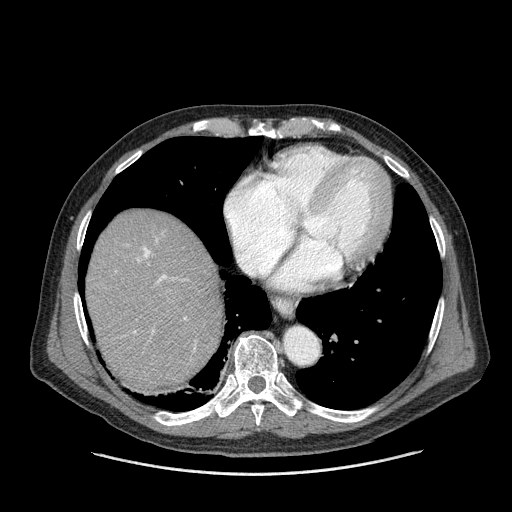
Contrast-enhanced abdominal CT (liver protocol), one axial slice; position 138 of 180 along the scan axis; 120 kVp; one of 2 acquisitions stored at this slice position; soft-tissue window (W 400 / L 40 HU); 2.5 mm slice thickness; 512 × 512 image matrix, field of view 420 × 420 mm. From the clinical record (not read from this slice): diagnosis: hepatocellular carcinoma (patient treated with transarterial chemoembolisation; whether this scan precedes or follows treatment is not stated here); TNM stage (as recorded): Stage-II; Child-Pugh class: A; tumour differentiation: well differentiated; tumour nodularity: multinodular.
Annotated regions visible in this slice (semi-automatically segmented with operator editing):
- abdominal aorta: box from (x=285, y=329) to (x=319, y=364) px
- liver parenchyma outside the tumour (the mass and vessels are separate outlines, so this box may not span the whole liver): (x=86, y=208)–(x=222, y=392)
- mass: (x=165, y=289)–(x=177, y=304)
- liver vessels: (x=134, y=239)–(x=195, y=348)